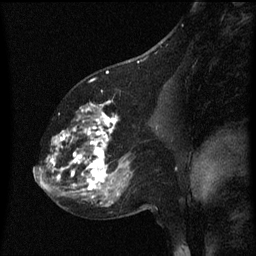
Breast MRI (dynamic contrast-enhanced), one sagittal slice. Slice 31 of 60 in the series (ordered by position). Dynamic contrast-enhanced series, image 2 of 3 at this slice position (ordered by acquisition). 1.5 T. TE 4.2 ms, TR 8 ms. 256 × 256 image matrix, field of view 200 × 200 mm. Patient: female, 60 years.
Outlined on this slice (semi-automatic segmentation, software-assisted and operator-edited):
- analysis volume of interest (the breast-tissue region the enhancement analysis was run in; not a lesion): box from (x=49, y=100) to (x=158, y=197) px
- tumour enhancement mask (voxels above the 70 % enhancement threshold inside the analysis volume of interest): (x=49, y=100)–(x=129, y=197)